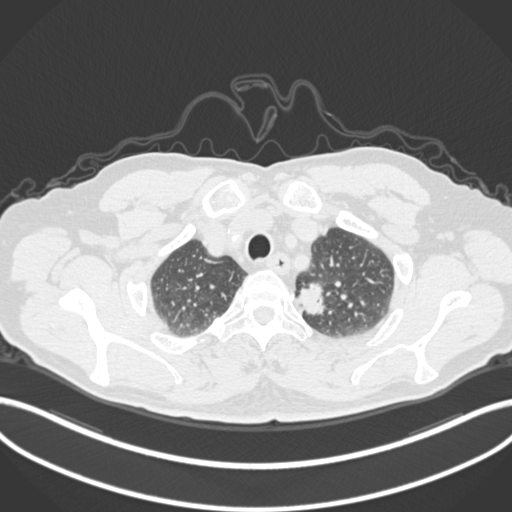
Chest CT, one axial slice. 120 kVp. Lung window (W 1500 / L -600 HU). 1 mm slice thickness. 512 × 512 image matrix. Patient: male, 64 years. Case-level facts recorded for this patient, not image findings: clinical TNM (as recorded): T1c N0 M0.
Outlined on this slice (rectangle marked by the reading radiologist):
- lung tumour (recorded histology: adenocarcinoma): box from (x=294, y=276) to (x=330, y=321) px